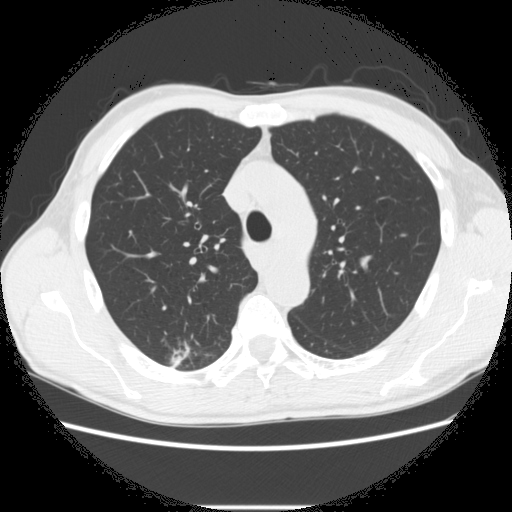
Low-dose screening chest CT, one axial slice; position 204 of 282 along the scan axis; 120 kVp; lung window (W 1500 / L -600 HU); 2.5 mm slice thickness; 512 × 512 image matrix, field of view 360 × 360 mm.
Structures marked on this image (manually delineated by an expert):
- lesion 1 (tumor, upper lobe of right lung): box from (x=170, y=343) to (x=189, y=368) px